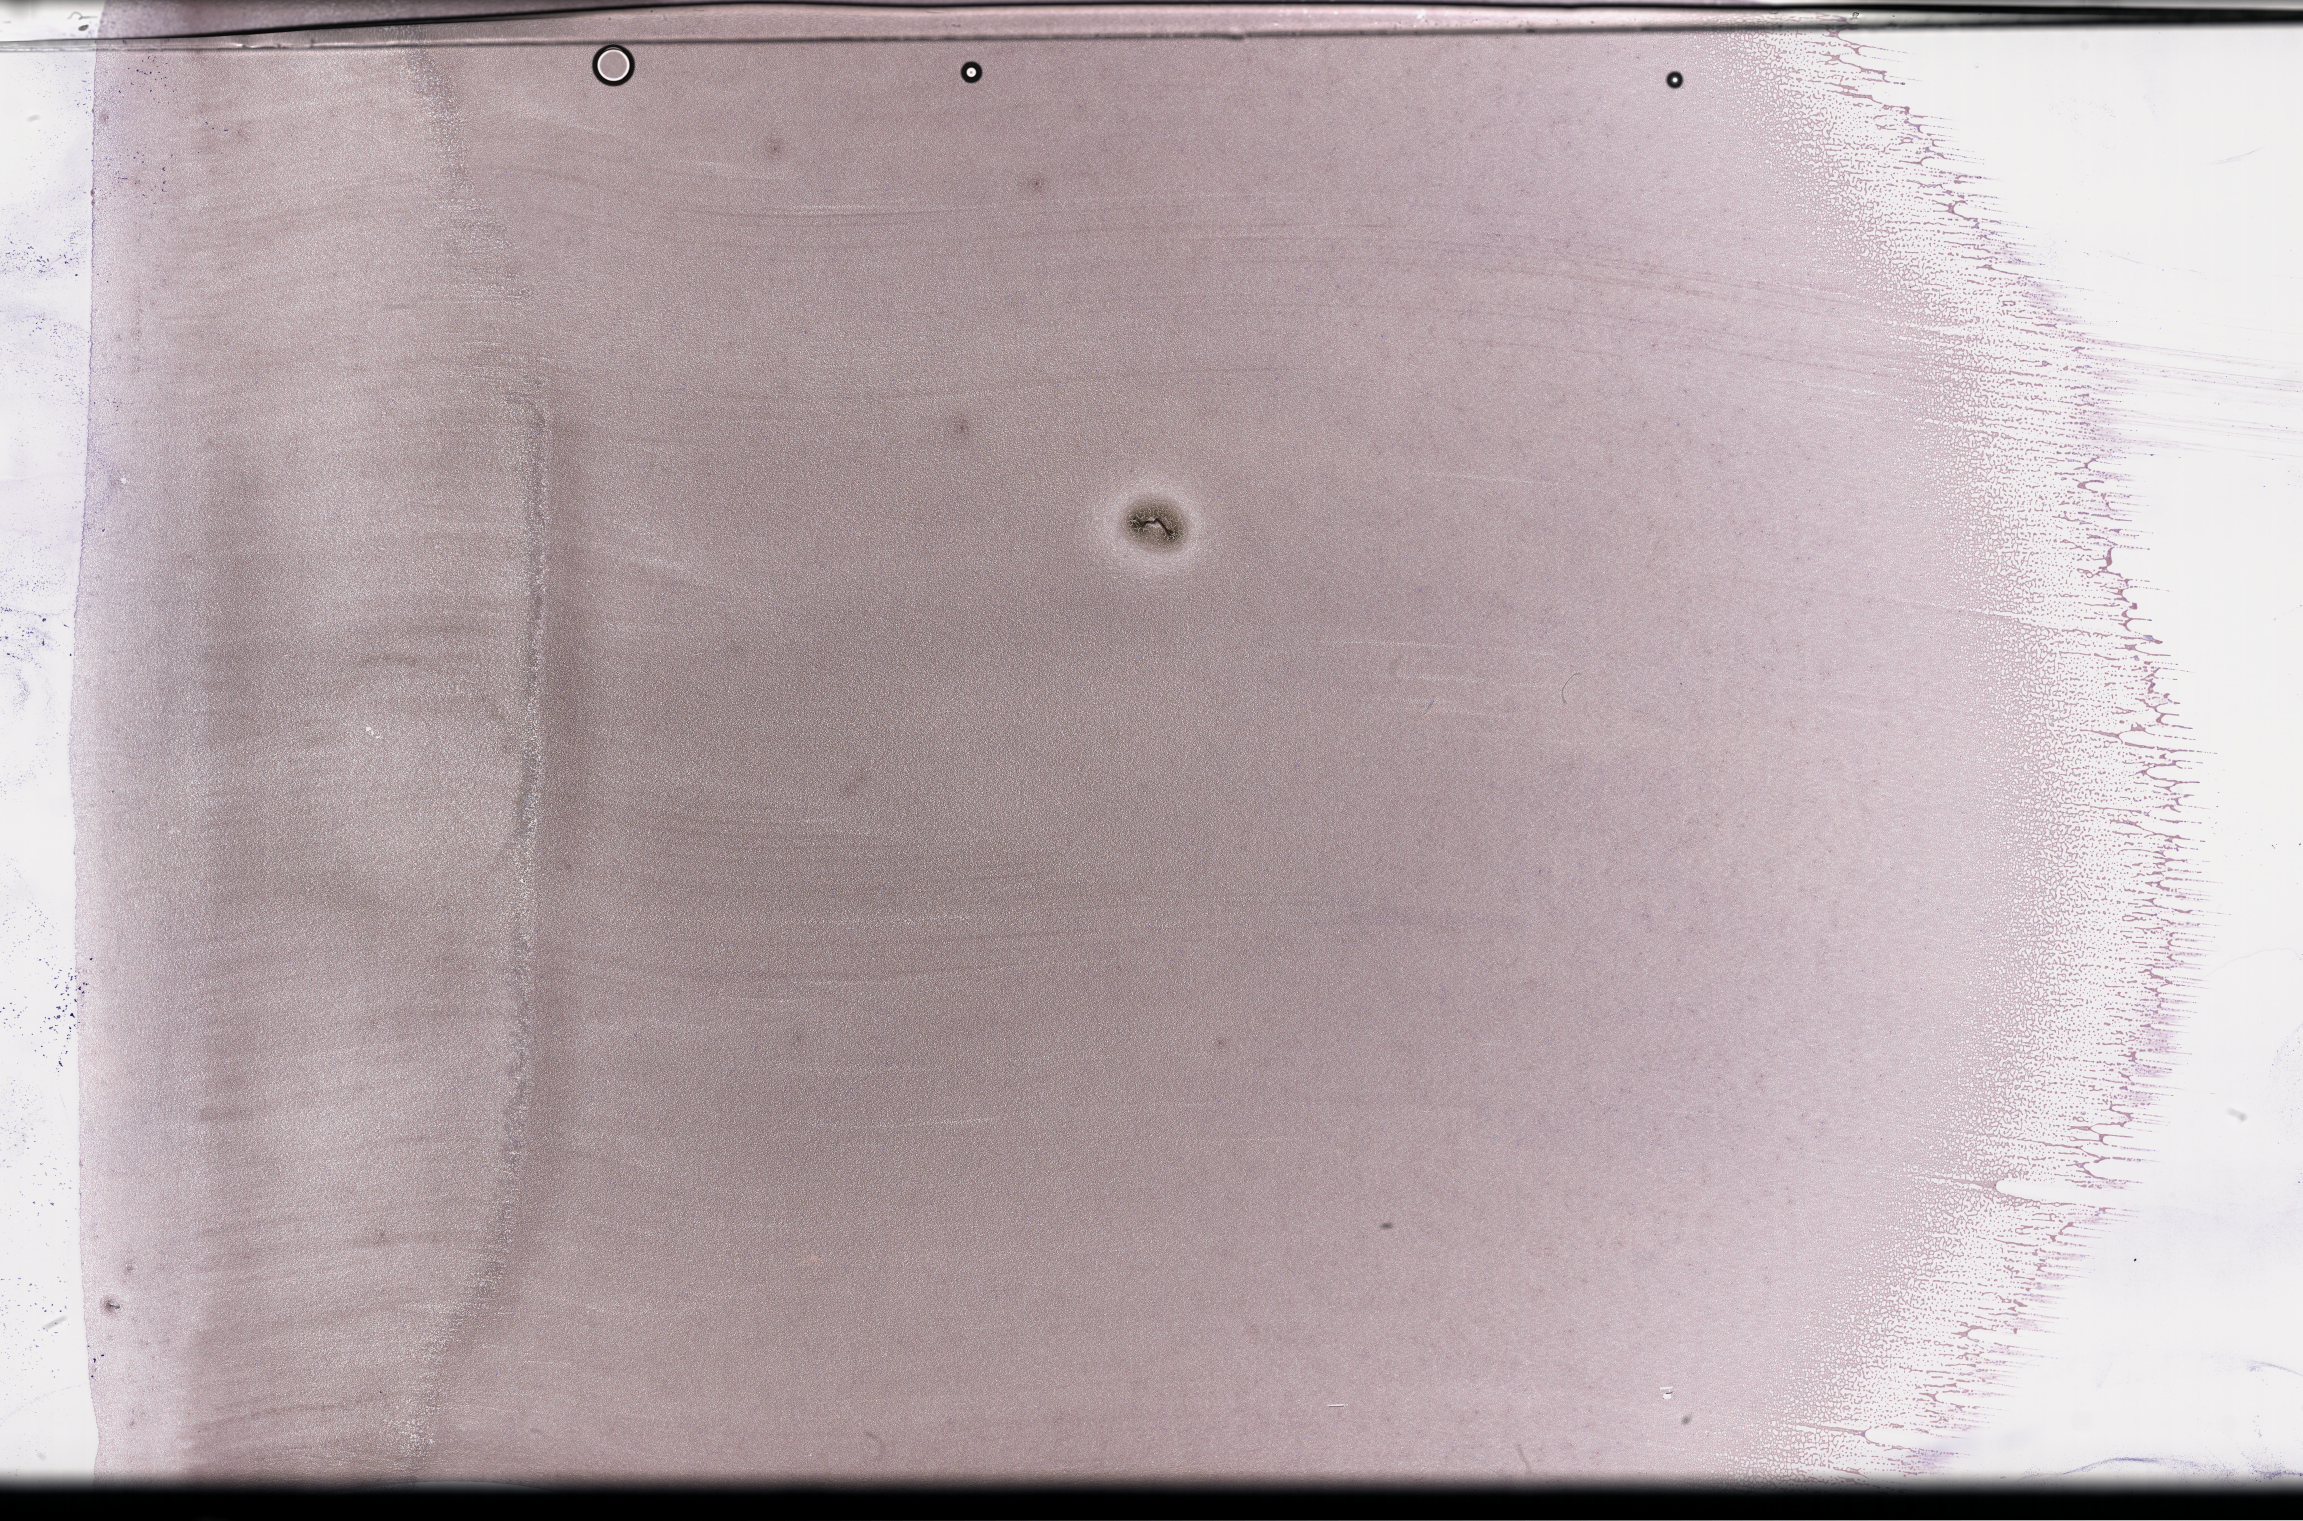
Wright-Giemsa-stained whole blood smear, whole-slide image — low-resolution overview of the scanned area, about 37.2 x 24.6 mm, EDTA-anticoagulated smear, collected on treatment. Patient sex: female.
- patient diagnosis: Plasma Cell Myeloma